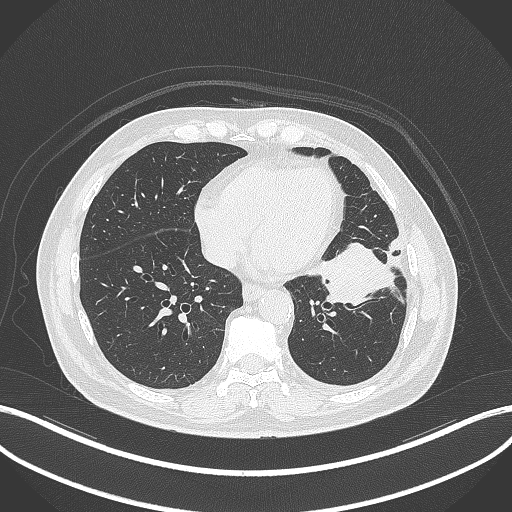
Chest CT, one axial slice; position 125 of 230 along the scan axis; reconstruction kernel B70f; 120 kVp; lung window (W 1500 / L -600 HU); 1 mm slice thickness; 512 × 512 image matrix, field of view 400 × 400 mm. Patient: male, 68 years. Case-level facts recorded for this patient, not image findings: clinical TNM (as recorded): T2b N0 M0.
Outlined on this slice (rectangle marked by the reading radiologist):
- lung tumour (recorded histology: squamous cell carcinoma): bounding box <307,245,401,311> (left, top, right, bottom; pixels)